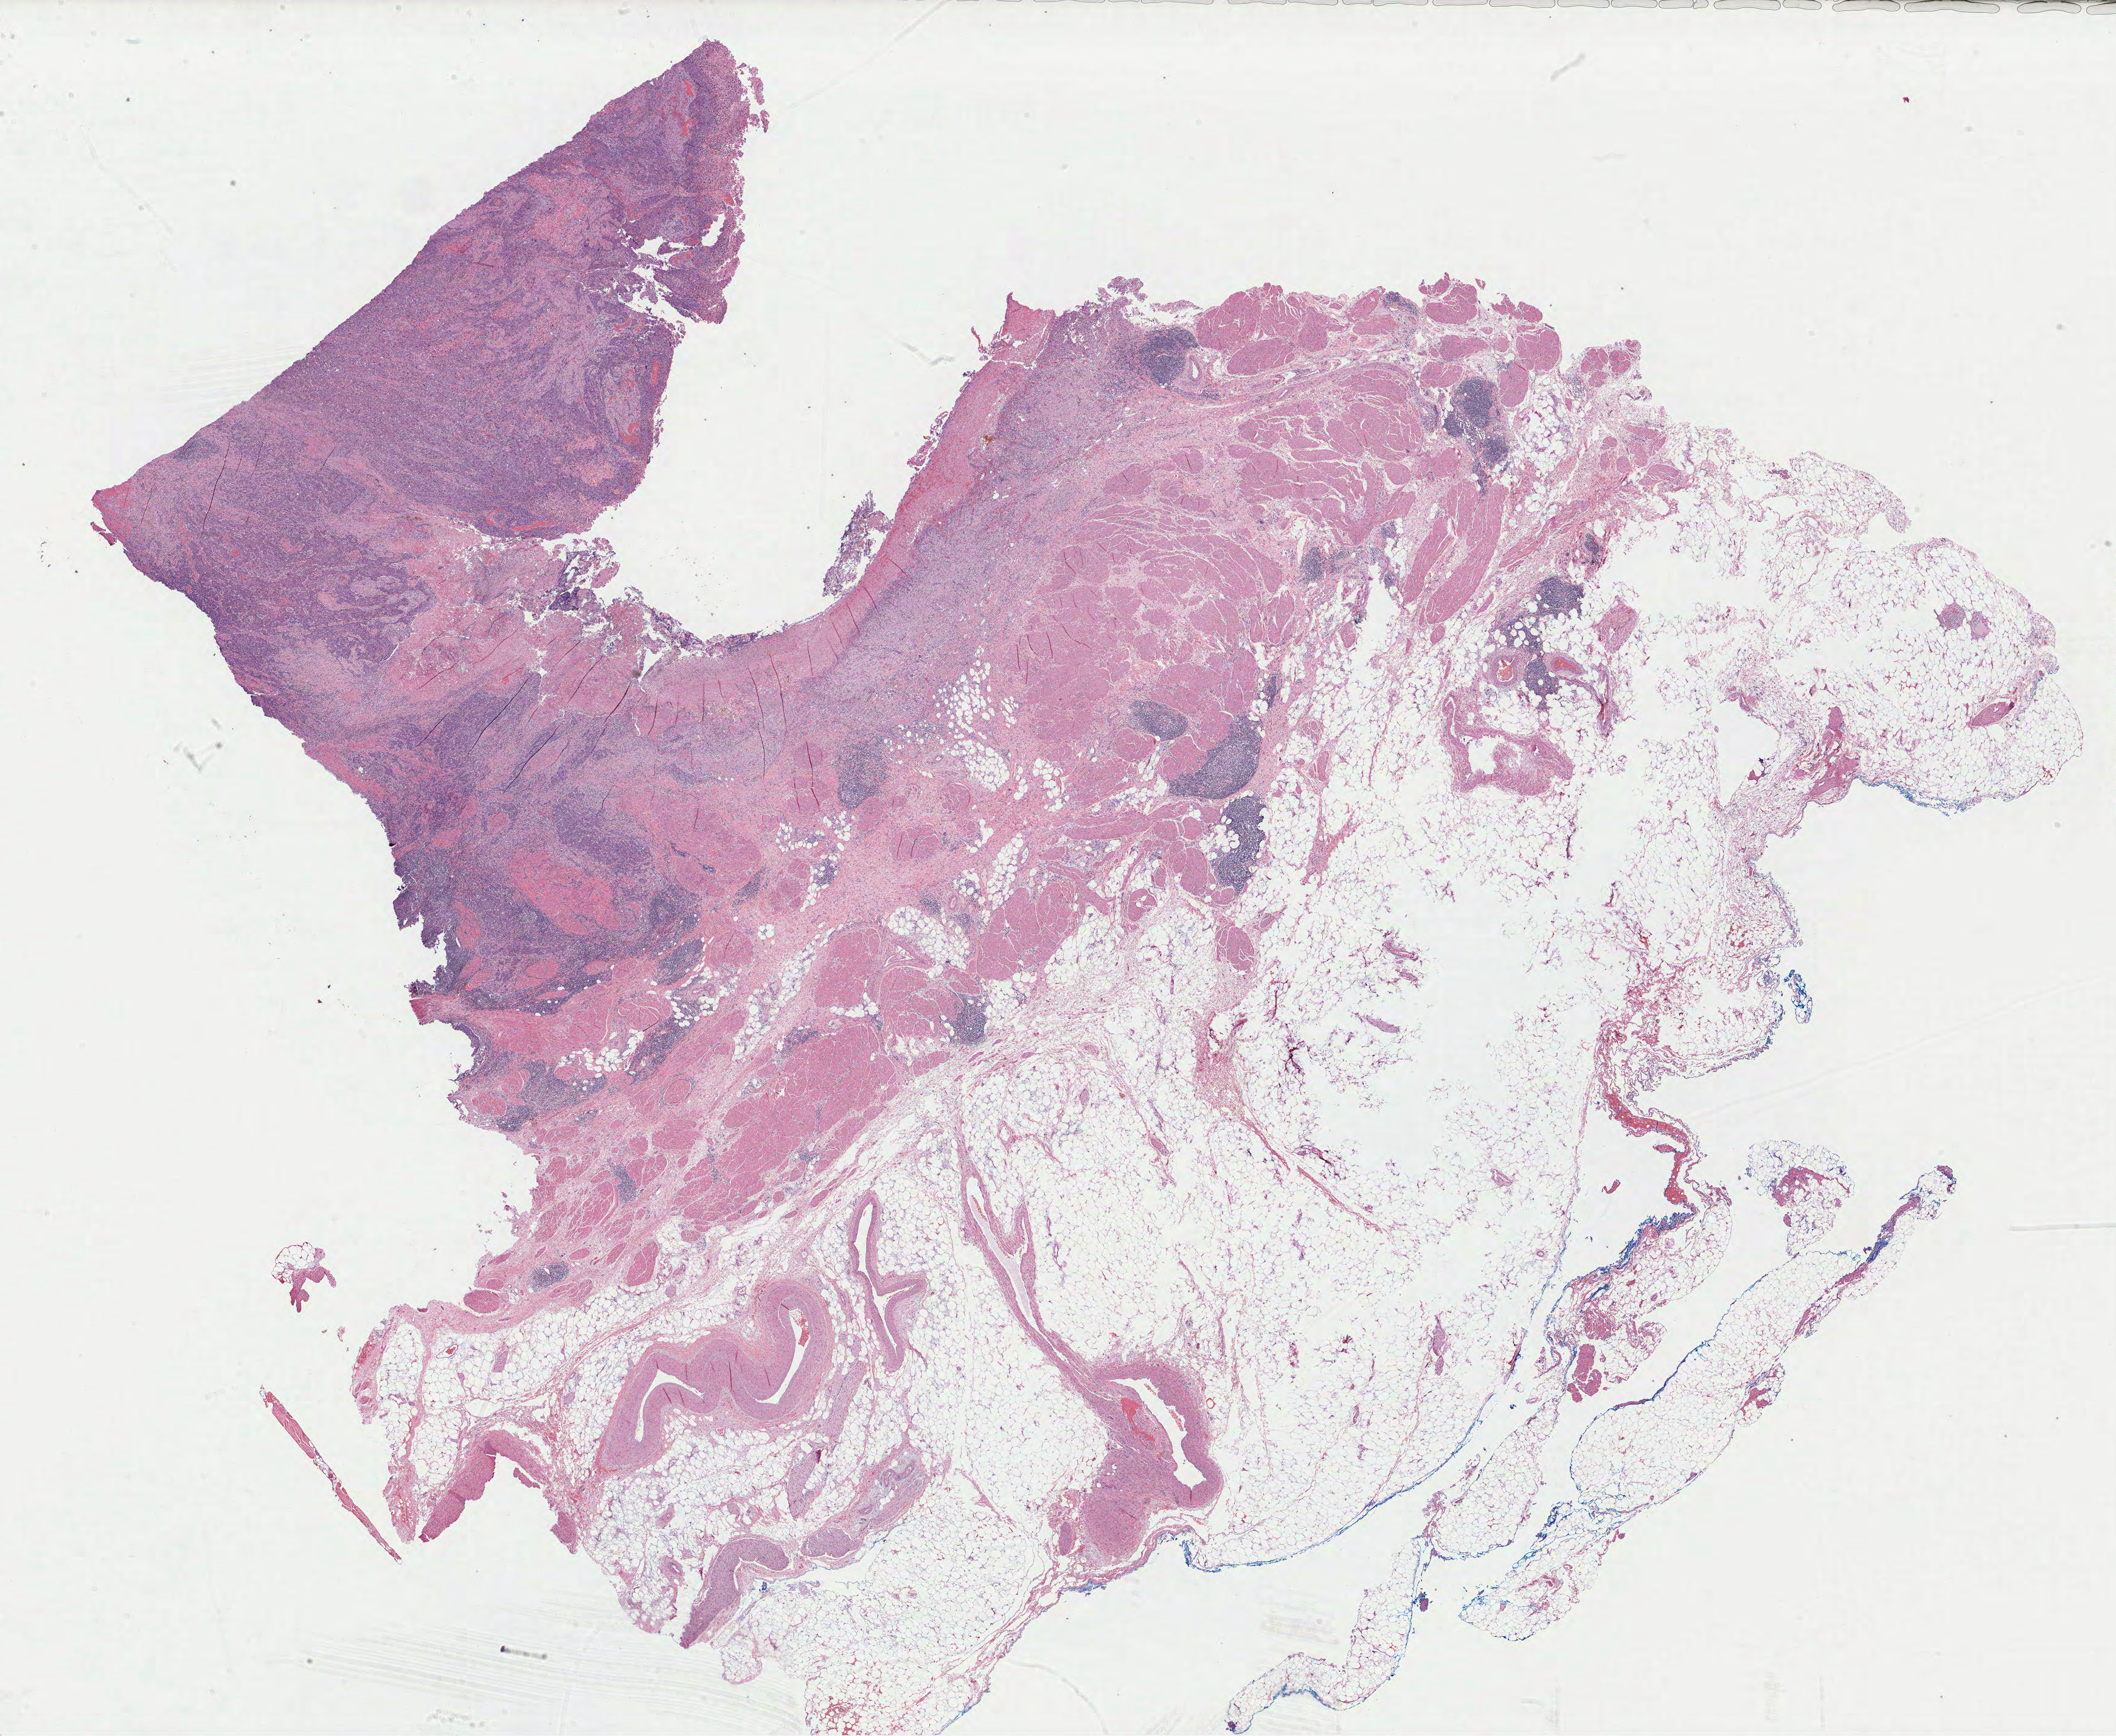
Digitized Hematoxylin and eosin (H&E) stained tissue section (whole slide) — low-resolution overview of the scanned area, about 28.0 x 23.0 mm, FFPE section, bladder, primary tumour sample. Male patient; age at initial diagnosis 70 years. Histologic grade: high grade.
AJCC pathologic stage: II (7th edition). Diagnosis: Transitional cell carcinoma. Lymph nodes positive (case pathology): 0 of 28 examined.